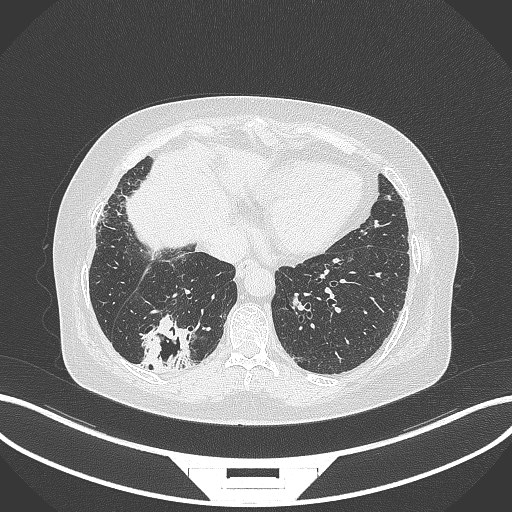
Chest CT, one axial slice; slice 56 of 296 in the series (ordered by position); 120 kVp; lung window (W 1500 / L -600 HU); 1 mm slice thickness; 512 × 512 image matrix, field of view 400 × 400 mm. Patient: female, 65 years. From the clinical record (not read from this slice): clinical TNM (as recorded): T2b N1 M0; histopathological grade: G1.
Outlined on this slice (bounding box drawn by a radiologist):
- lung tumour (recorded histology: adenocarcinoma): bounding box <132,313,197,375> (left, top, right, bottom; pixels)